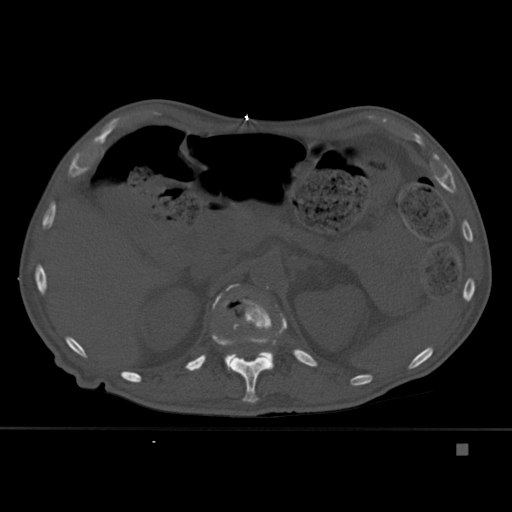
CT including the spine, one axial slice; slice 195 of 451 in the series (ordered by position); bone window (W 1800 / L 400 HU); 512 × 512 image matrix. Patient: male, 75 years. Case-level facts recorded for this patient, not image findings: primary cancer: prostate.
Structures marked on this image (semi-automatic segmentation, software-assisted and operator-edited):
- L1 vertebra: bounding box (x1, y1, x2, y2) in pixels: (213, 284, 274, 371)
- T12 vertebra: (212, 299, 287, 403)